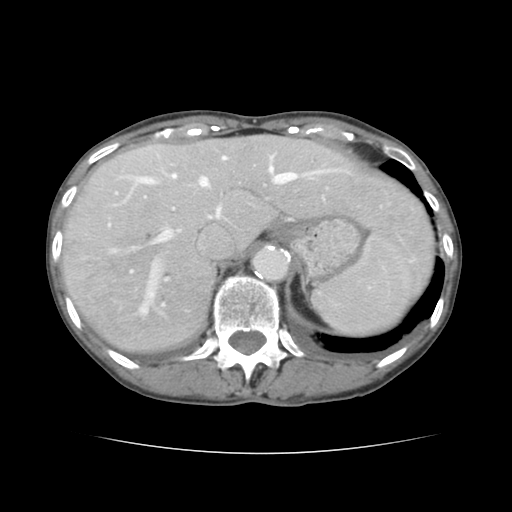
Contrast-enhanced abdominal CT, one axial slice; slice 107 of 136 in the series (ordered by position); 120 kVp; intravenous contrast given; soft-tissue window (W 400 / L 40 HU); 512 × 512 image matrix. Female patient, age 77 years. Case-level facts recorded for this patient, not image findings: diagnosis: colorectal cancer liver metastases, imaged before liver resection; multiple liver metastases: yes; largest metastasis: 3 cm; disease in both lobes: no.
Structures marked on this image (outlined manually by an expert reader):
- hepatic veins: bounding box (x1, y1, x2, y2) in pixels: (110, 156, 339, 314)
- liver: (62, 136, 434, 354)
- planned liver remnant (the part of the liver to remain after resection): (163, 136, 434, 274)
- portal vein (with intrahepatic branches): (109, 174, 383, 280)